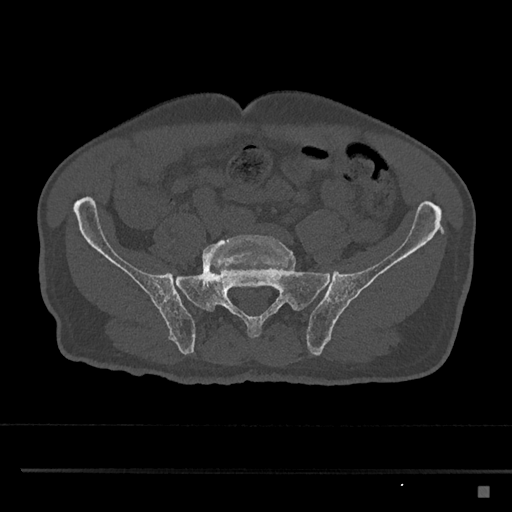
CT including the spine, one axial slice. Position 547 of 797 along the scan axis. Reconstruction kernel Br40s/3. 120 kVp. Bone window (W 1800 / L 400 HU). 0.5 mm slice thickness. 512 × 512 image matrix, field of view 391 × 391 mm. Male patient, age 59 years. From the clinical record (not read from this slice): primary cancer: prostate.
Annotated regions visible in this slice (semi-automatically segmented with operator editing):
- L5 vertebra: bounding box (x1, y1, x2, y2) in pixels: (202, 235, 292, 274)